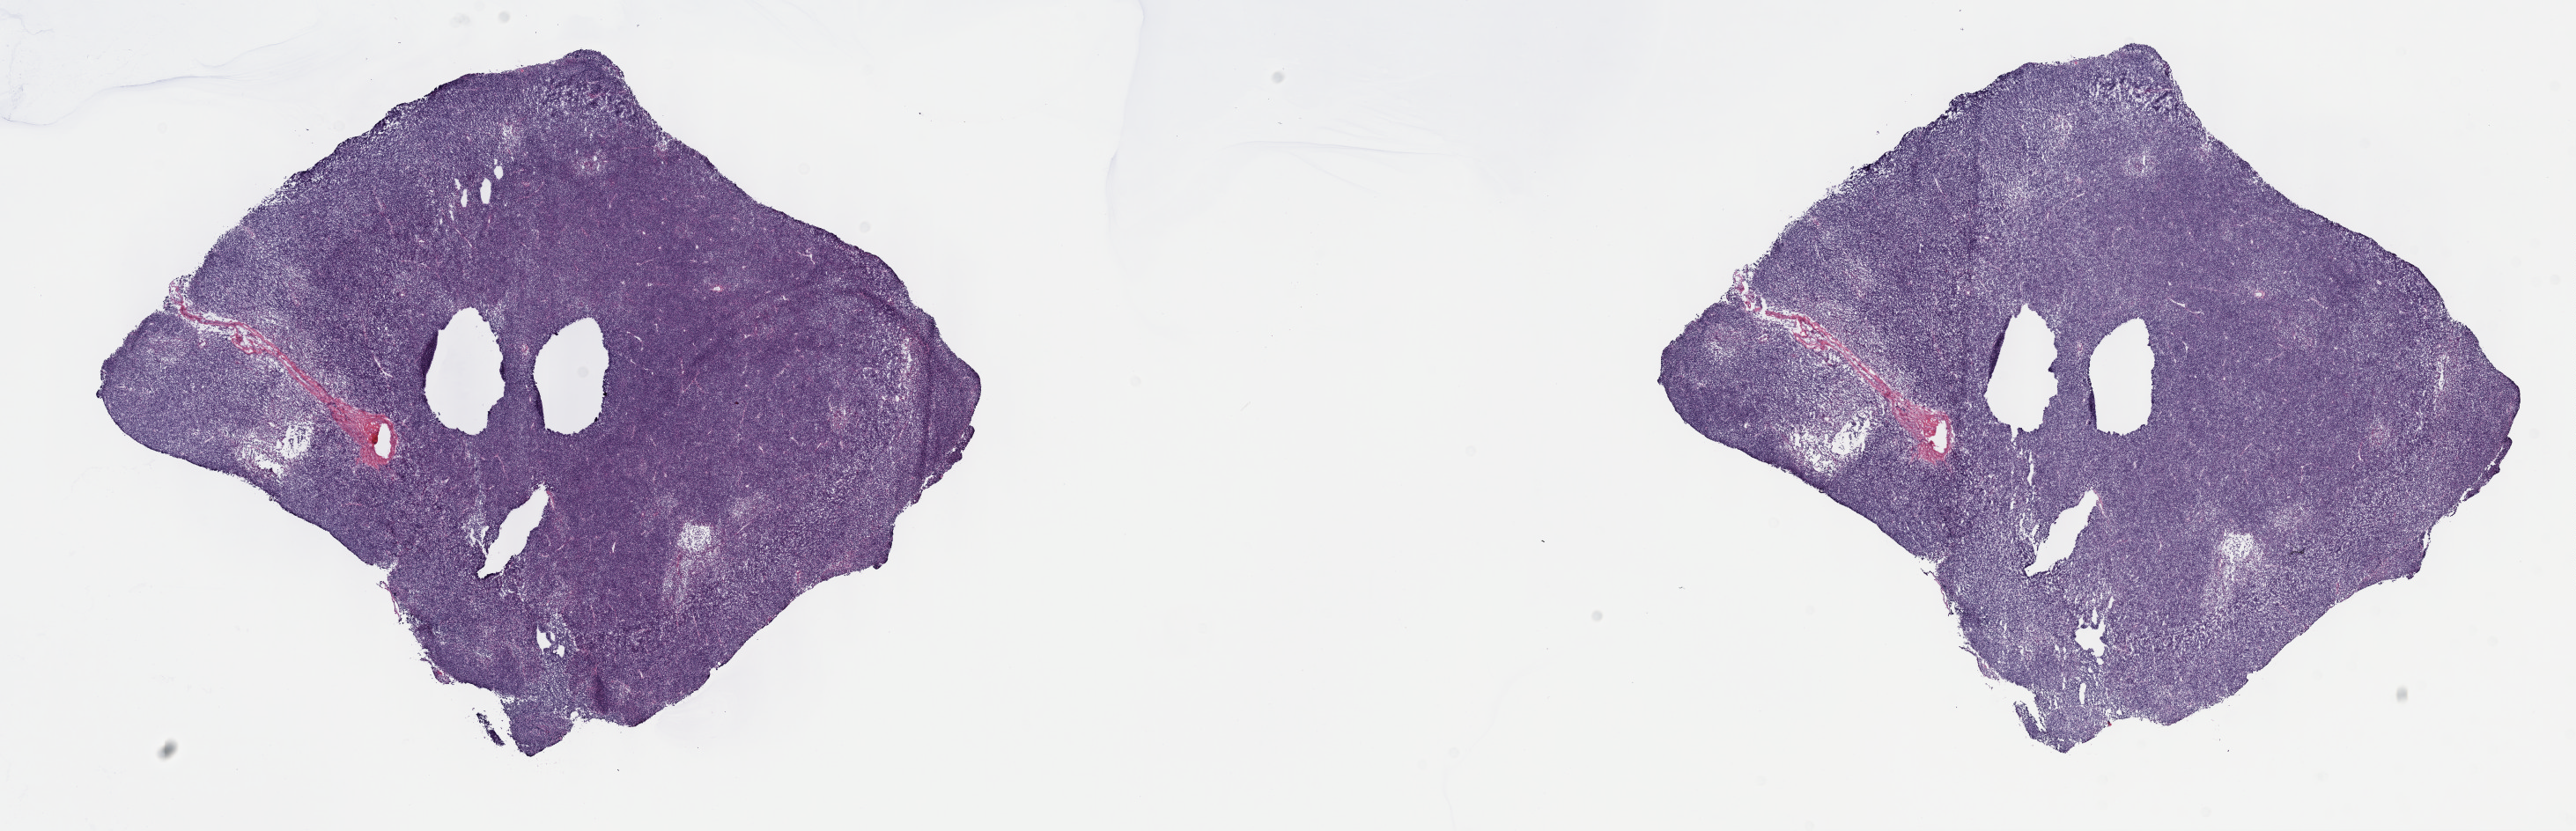
Whole-slide histology image, H&E-stained — a low-resolution overview of the entire scanned area, about 23.7 x 7.6 mm; frozen section from the top of the tissue portion; sample: primary tumour, thymus. Male patient; age at initial diagnosis 59 years. Composition of this section per pathologist review: tumour cells 100%, tumour nuclei 98%, normal cells 0%, stromal cells 0%, necrosis 0%. Inflammatory infiltration, as recorded: lymphocyte infiltration 0%, monocyte infiltration 0%, neutrophil infiltration 0%.
* histologic diagnosis: Thymoma, type AB, malignant